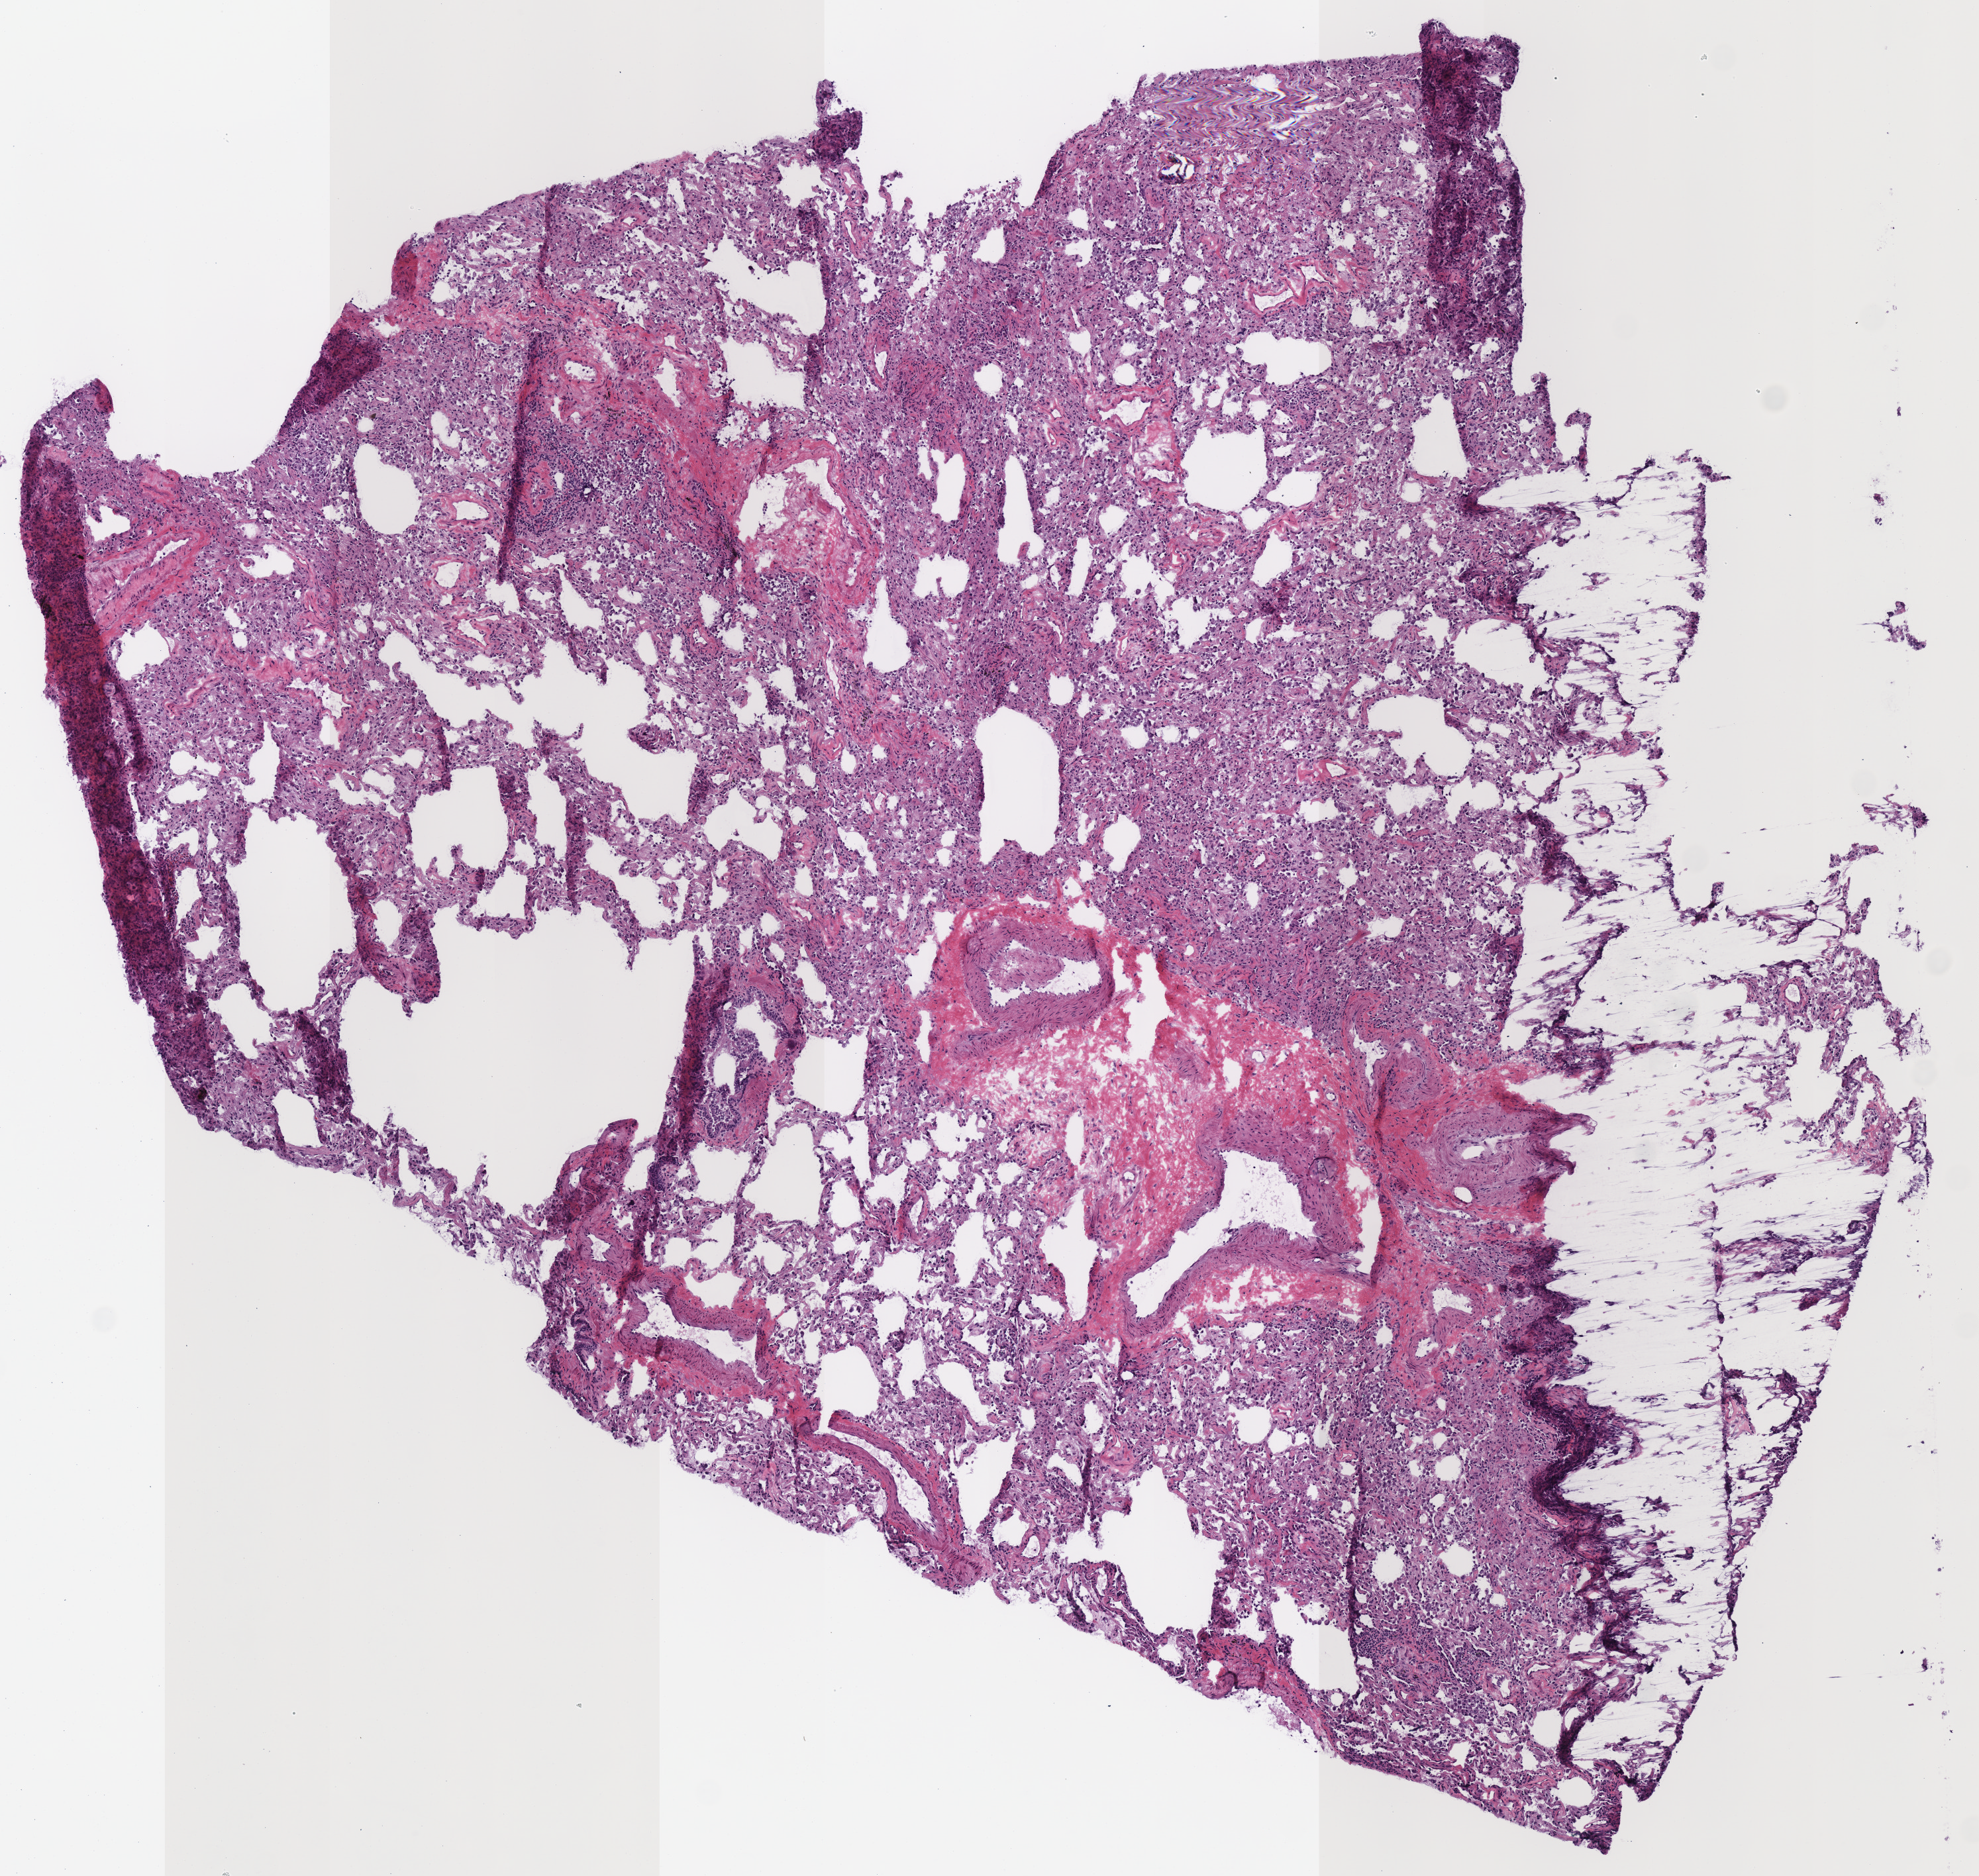
Whole-slide histology image, Hematoxylin and eosin (H&E) stained, shown as a low-resolution overview of the whole scanned area (about 5.9 x 5.6 mm, acquisition: 40x scan); frozen section from the top of the tissue portion; lung, solid tissue normal (non-tumour tissue) sample. Male, age 55 years at initial diagnosis. Infiltration values recorded for this section: lymphocyte infiltration 15%, monocyte infiltration 20%.
* this section: solid tissue normal sample (biorepository sample class)
* patient diagnosis: Adenocarcinoma with mixed subtypes (lower lobe, lung)